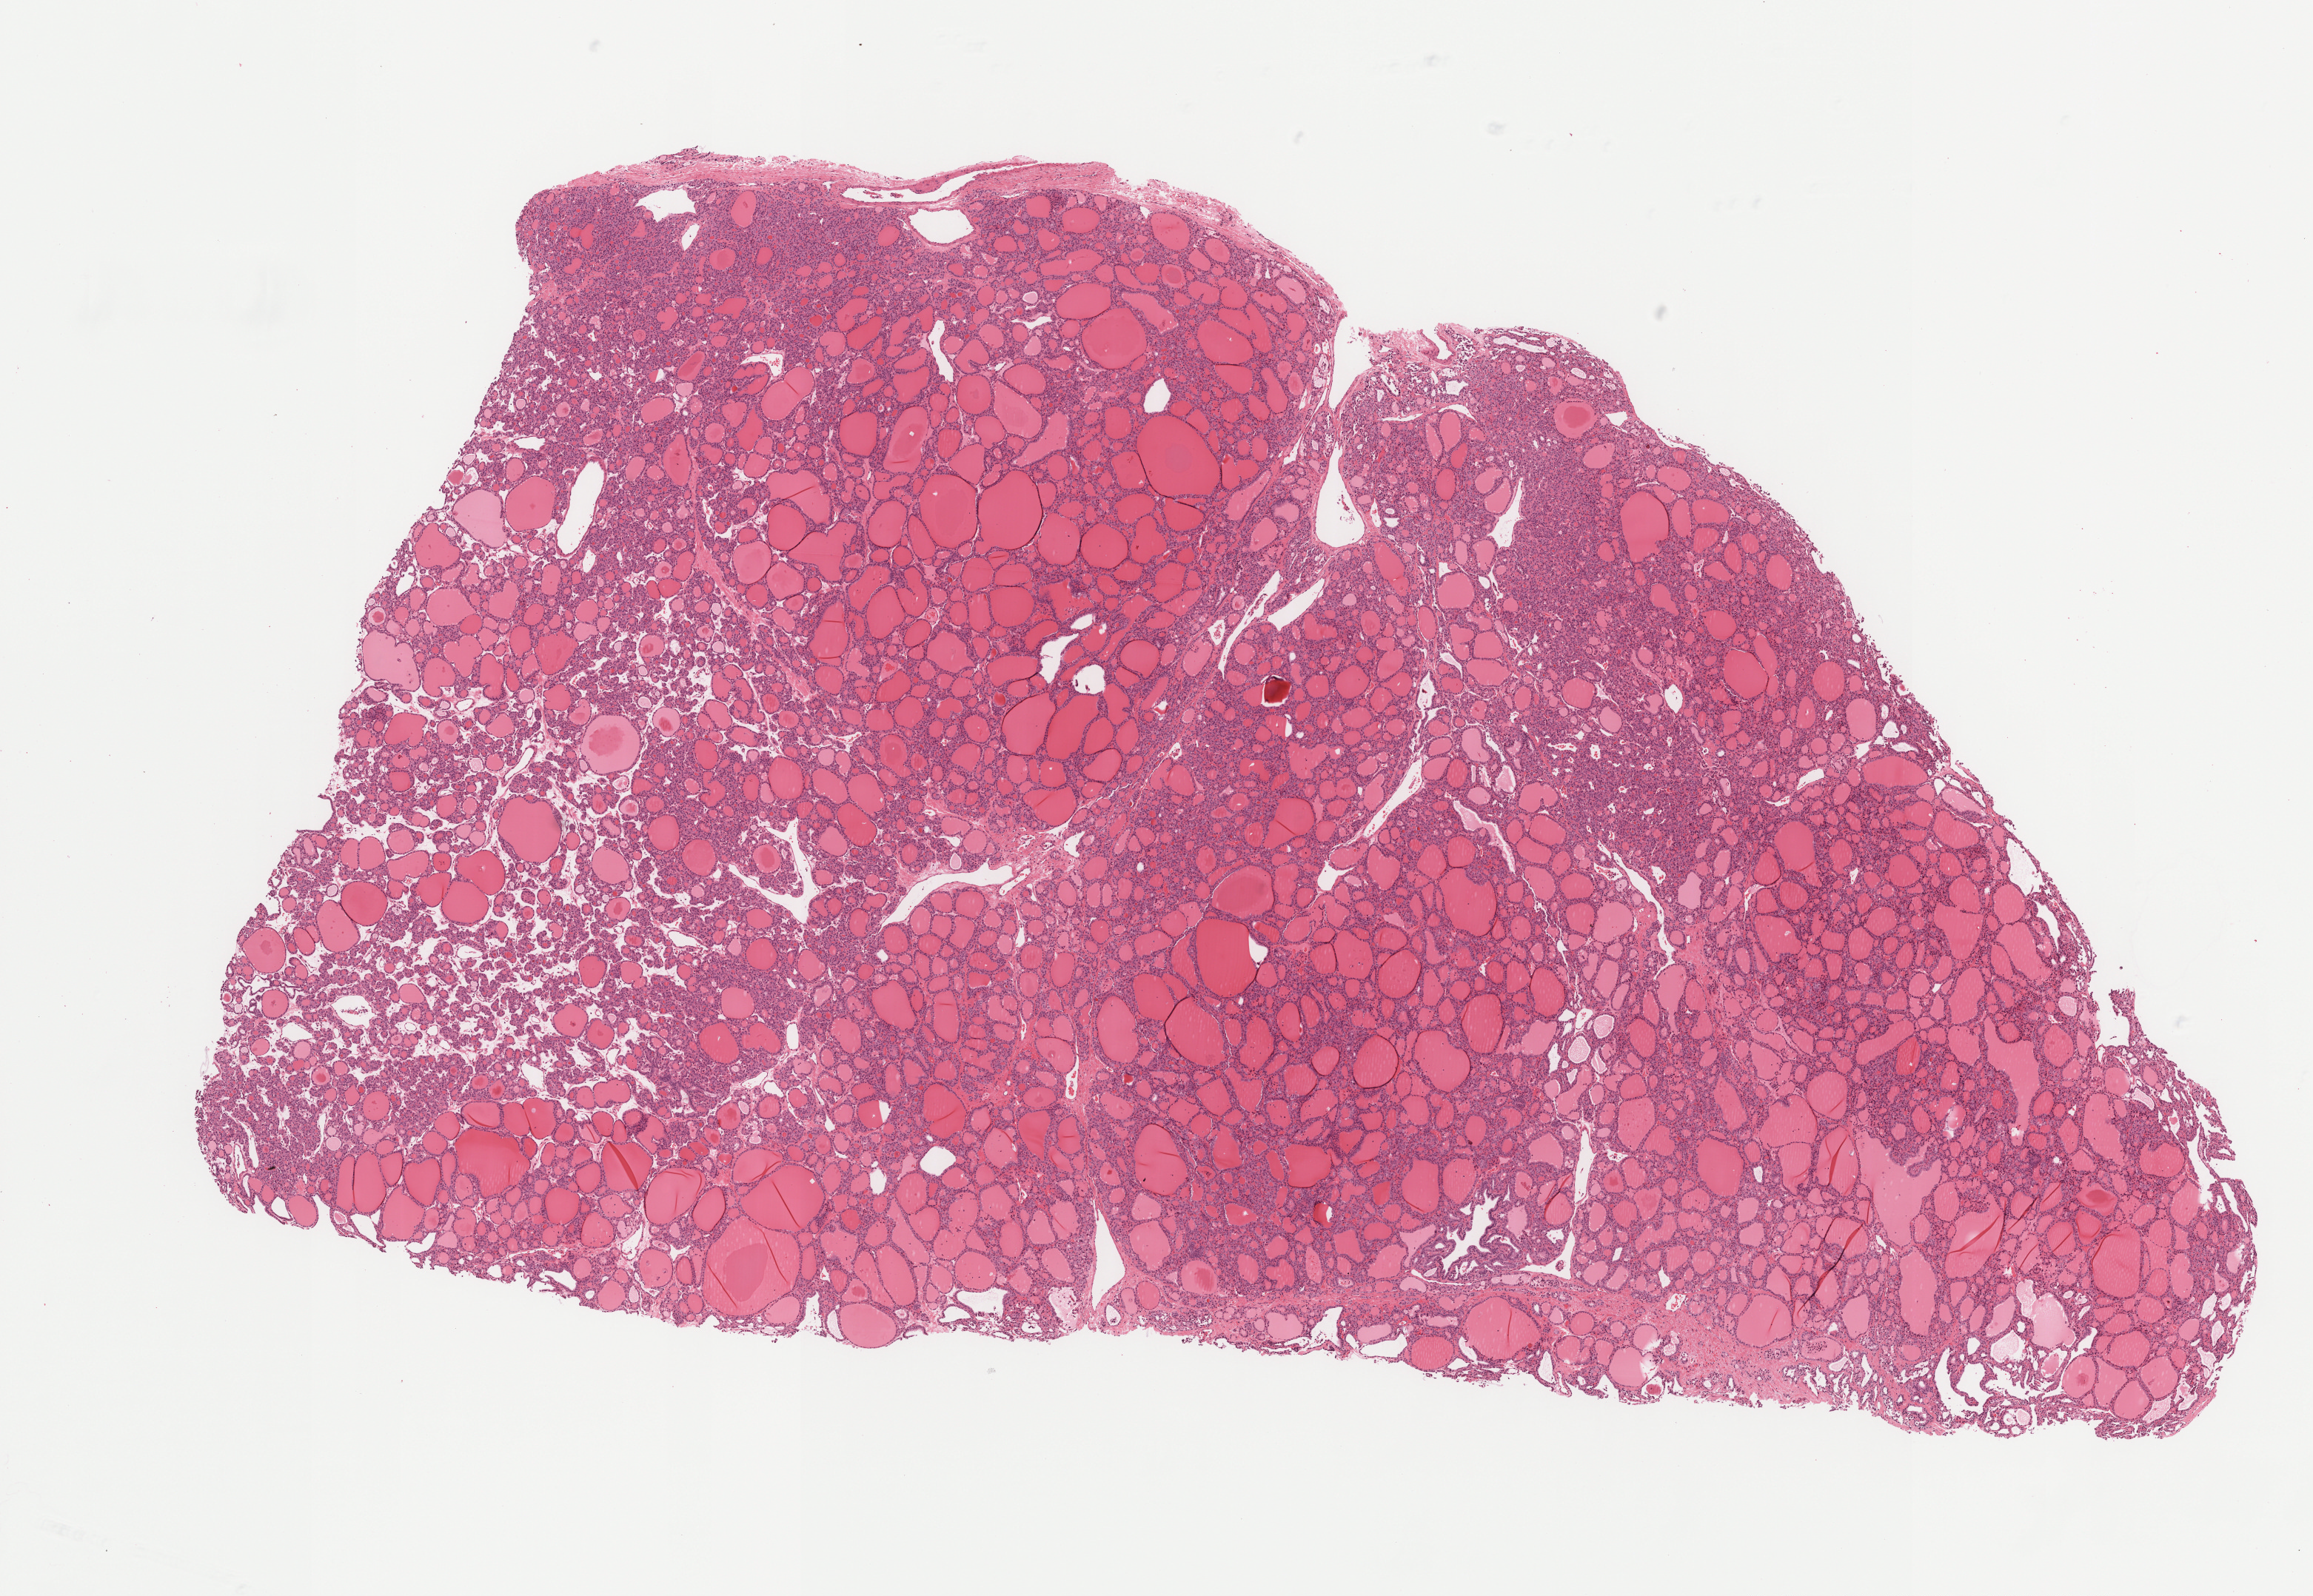
Whole-slide histology image, Hematoxylin and eosin (H&E) stained — low-resolution overview of the scanned area, about 12.6 x 8.7 mm, FFPE section, primary tumour sample from the thyroid. Male patient; age at initial diagnosis 28 years.
- histologic diagnosis: Papillary carcinoma, follicular variant
- laterality: right
- TNM: T2 N1b MX
- AJCC pathologic stage: I (7th edition)